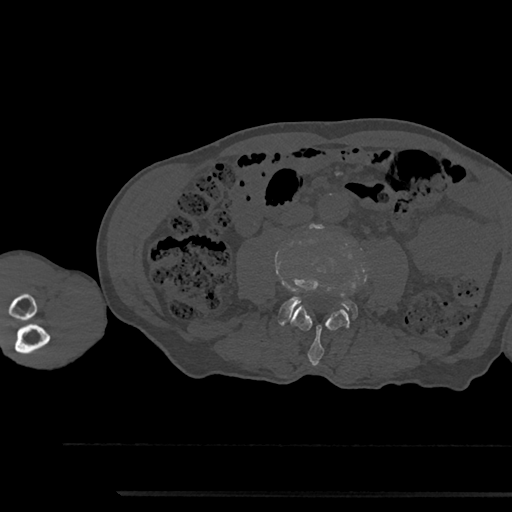
CT including the spine, one axial slice; position 451 of 797 along the scan axis; reconstruction kernel Br40s/3; 120 kVp; bone window (W 1800 / L 400 HU); 512 × 512 image matrix, field of view 367 × 367 mm. Patient: male, 79 years. Case-level facts recorded for this patient, not image findings: primary cancer: prostate.
Outlined on this slice (semi-automatically segmented with operator editing):
- L3 vertebra: bounding box <291,306,349,366> (left, top, right, bottom; pixels)
- L4 vertebra: <278,279,357,325>